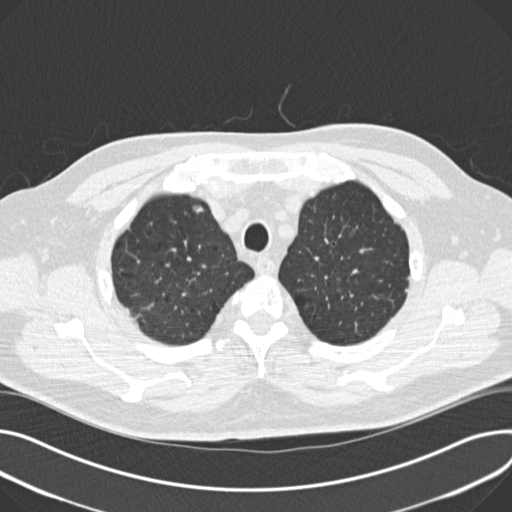
Low-dose screening chest CT, one axial slice; slice 151 of 180 in the series (ordered by position); lung window (W 1500 / L -600 HU); 2 mm slice thickness; 512 × 512 image matrix.
Annotated regions visible in this slice (manually delineated by an expert):
- lesion 2 (tumor, upper lobe of right lung): bounding box (x1, y1, x2, y2) in pixels: (193, 206, 203, 212)